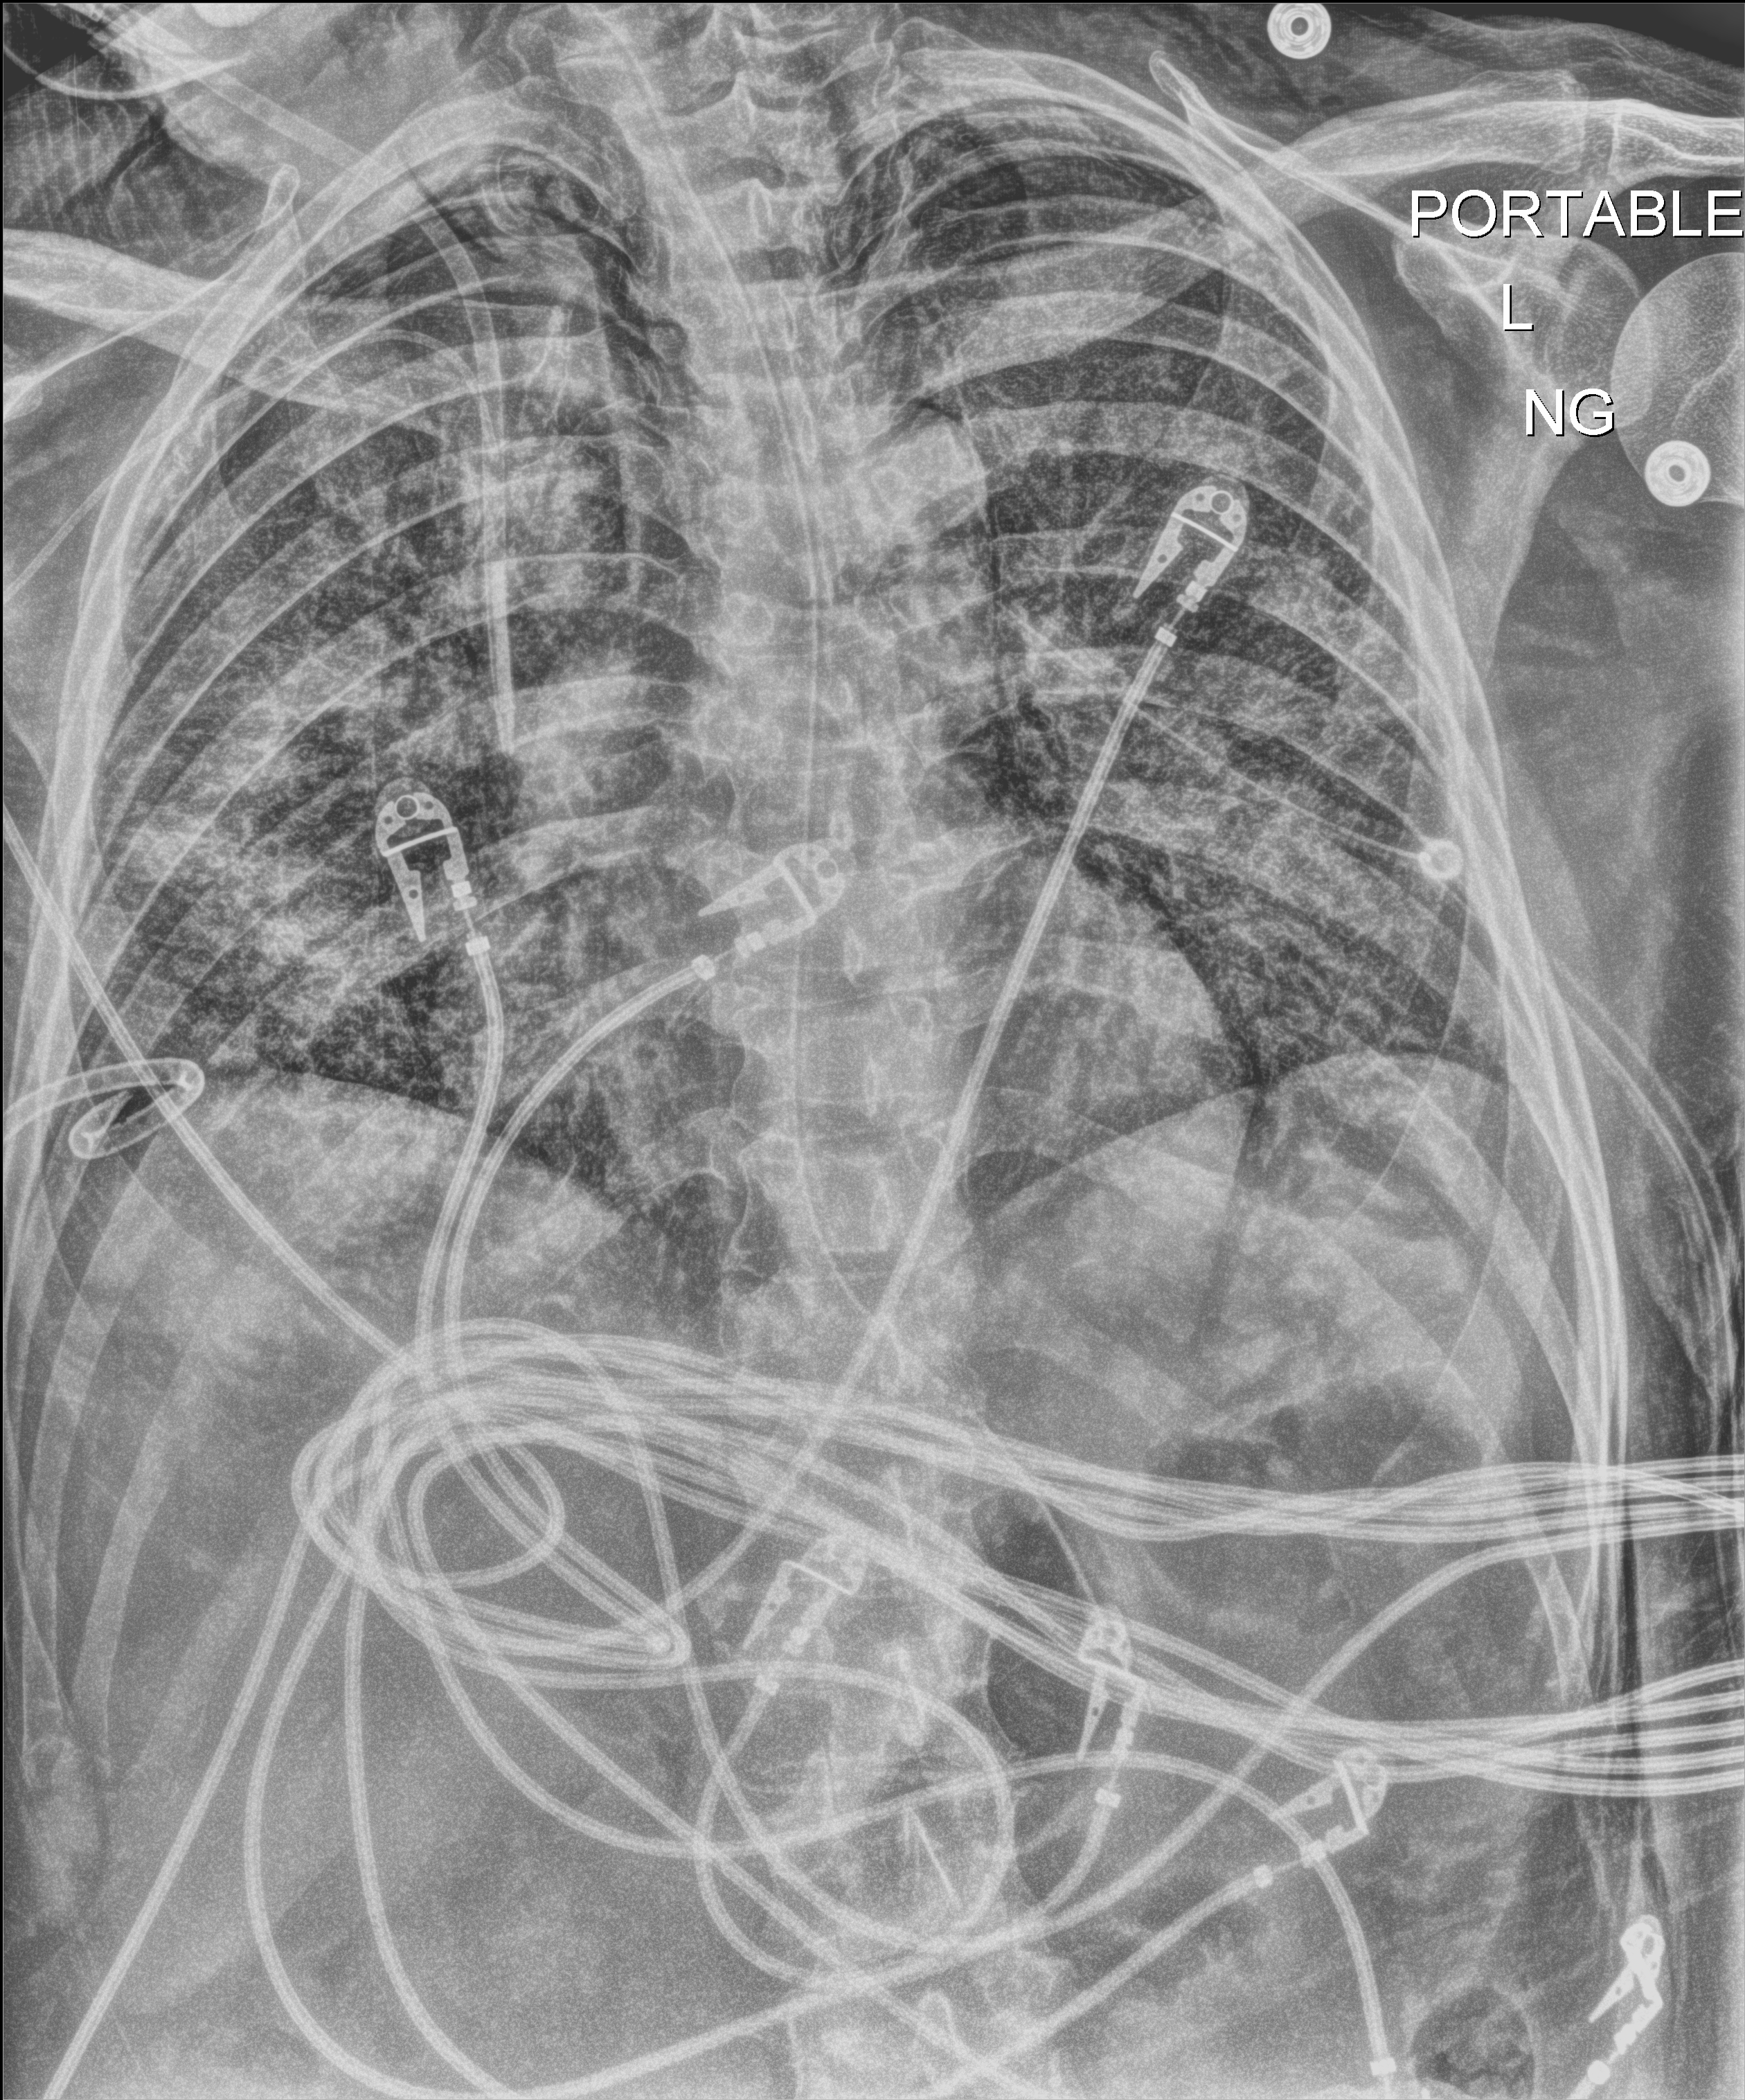
Chest X-ray (portable); anteroposterior (AP) projection. Male patient hospitalised with COVID-19, age 18–59 years.
Hospital-stay facts (about this admission, not read from this image; timing relative to this image not recorded): hypertension (admission record): no; admitted to intensive care during this hospital stay: yes.